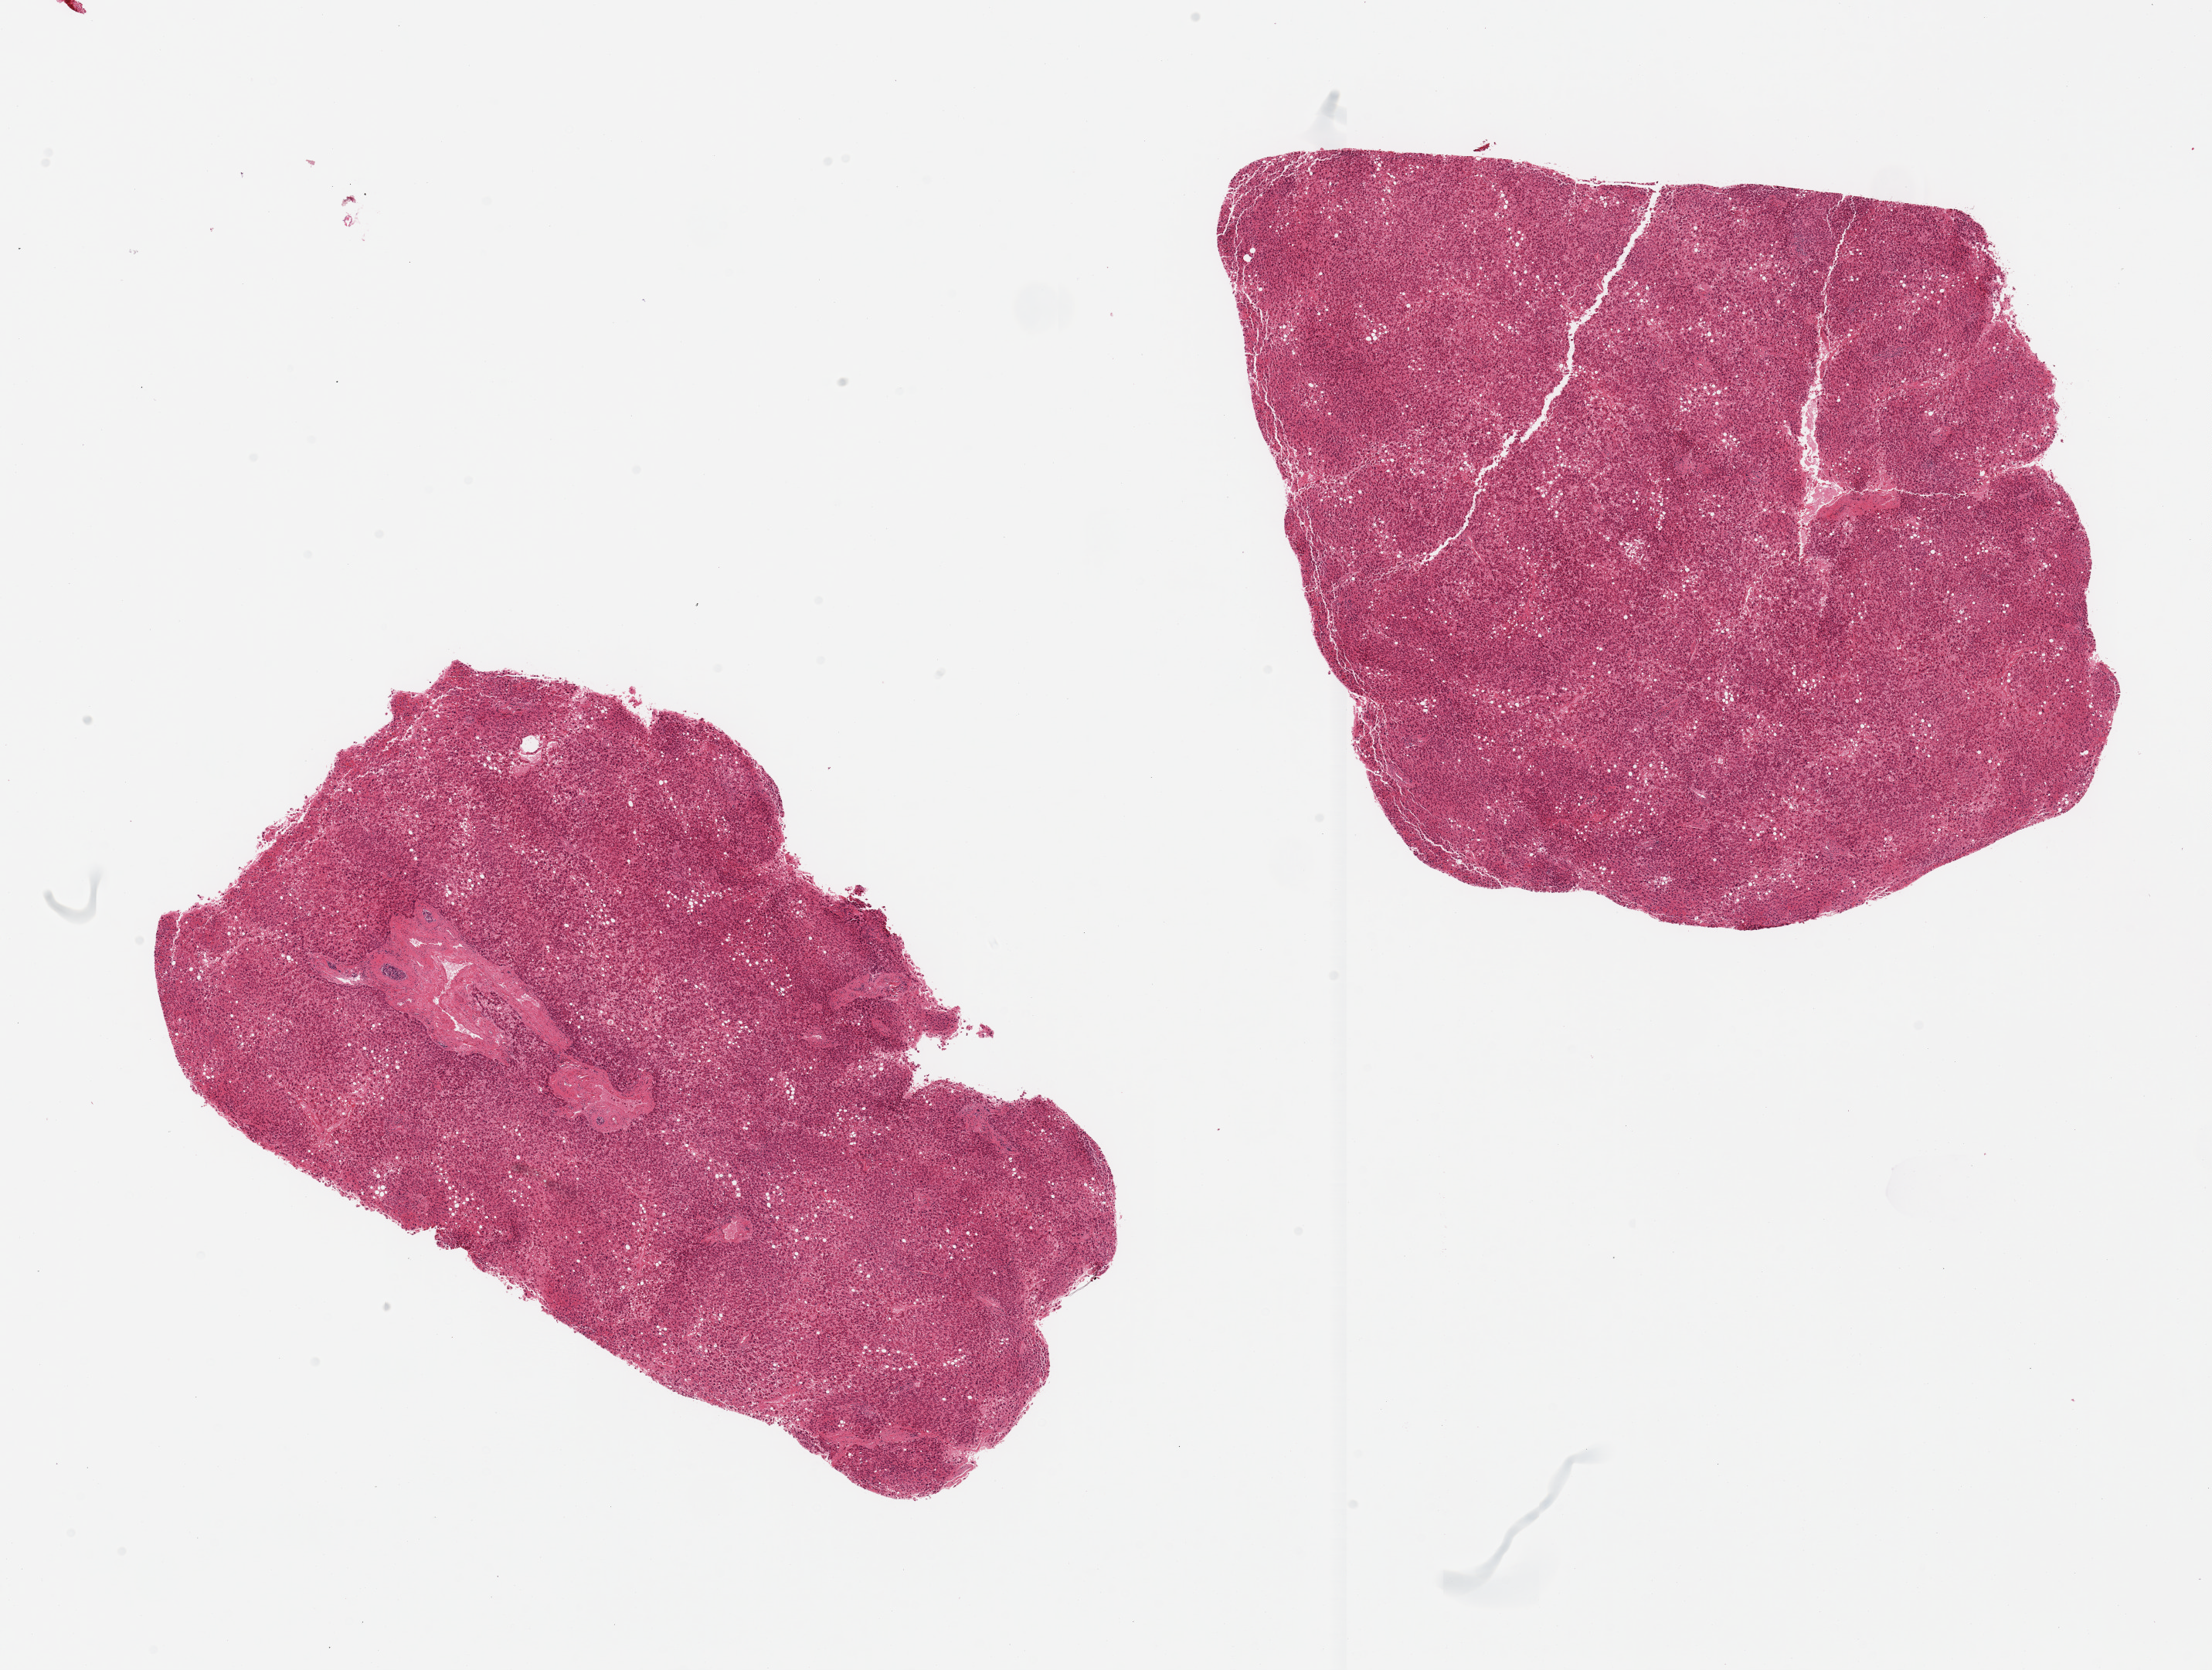
Haematoxylin and eosin whole-slide image, shown as a low-resolution overview of the whole scanned area (about 22.6 x 17.1 mm, from a 20x scan), PAXgene-fixed paraffin-embedded (PFPE) section, target tissue: liver, tissue donor sample.
Reviewer comment on this tissue sample: 2 pieces; 10% macrovesicular steatosis, moderate congestion.